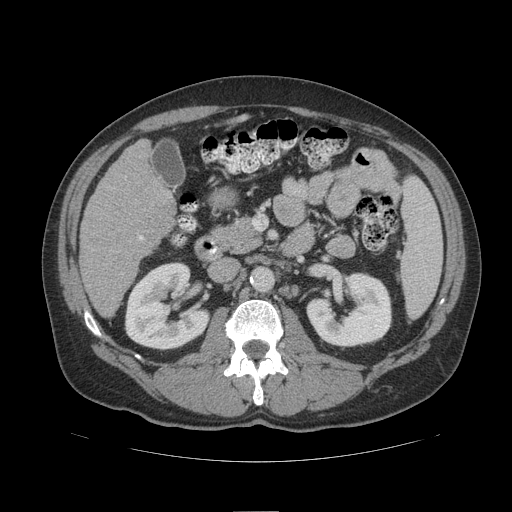
Contrast-enhanced abdominal CT (liver protocol), one axial slice; position 46 of 109 along the scan axis; soft-tissue window (W 400 / L 40 HU); 512 × 512 image matrix, field of view 420 × 420 mm. Case-level facts recorded for this patient, not image findings: diagnosis: hepatocellular carcinoma (patient treated with transarterial chemoembolisation; whether this scan precedes or follows treatment is not stated here); TNM stage (as recorded): Stage-IIIB; Child-Pugh class: A; tumour differentiation: poorly differentiated.
Outlined on this slice (semi-automatically segmented with operator editing):
- liver parenchyma outside the tumour (the mass and vessels are separate outlines, so this box may not span the whole liver): bounding box <80,140,174,316> (left, top, right, bottom; pixels)
- liver vessels: <139,235,143,240>